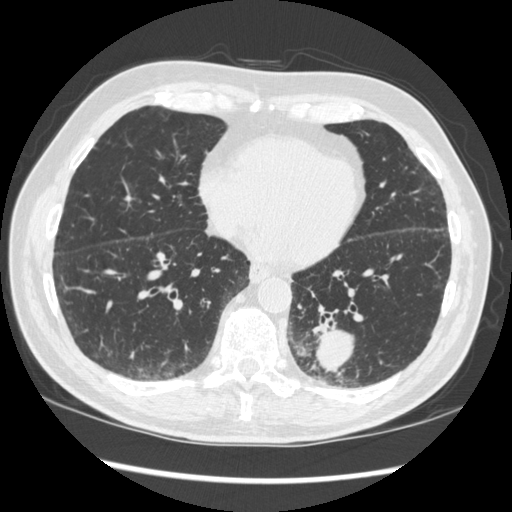
Chest CT (low-dose screening protocol), one axial image. Baseline screening round. Lung window (W 1500 / L -600 HU). 1.25 mm slice thickness. Slice 118 of 348 in the series. Male, age 72 years at enrolment. Current smoker at enrolment.
- Expert reader's lesion annotation, bounding box (x1, y1, x2, y2) in pixels: (274, 296, 378, 384).
- The screening reader recorded 2 non-calcified nodules or masses ≥4 mm on this exam (left lower lobe, right middle lobe); which of them this box marks is not recorded.
- Lung cancer was diagnosed 37 days after this screen: squamous cell carcinoma, NOS, left lower lobe, stage IIIA (AJCC 6th edition), 60 mm at pathology.